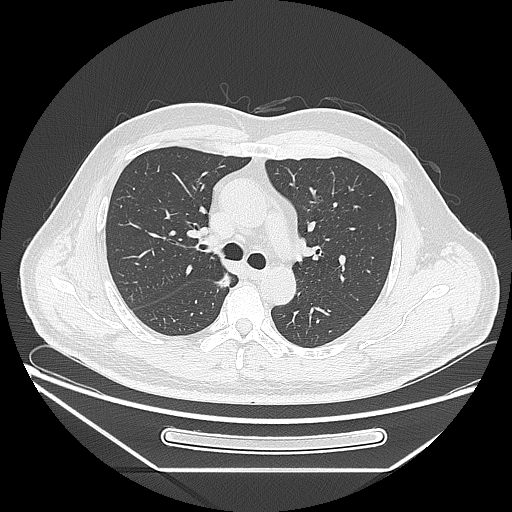
Chest CT, one axial slice; slice 166 of 271 in the series (ordered by position); reconstruction kernel LUNG; 120 kVp; lung window (W 1500 / L -600 HU); 512 × 512 image matrix, field of view 414 × 414 mm. Male patient, age 49 years. Case-level facts recorded for this patient, not image findings: clinical TNM (as recorded): T1b N0 M0; histopathological grade: G2.
Annotated regions visible in this slice (bounding box drawn by a radiologist):
- lung tumour (recorded histology: adenocarcinoma): box from (x=211, y=268) to (x=239, y=295) px